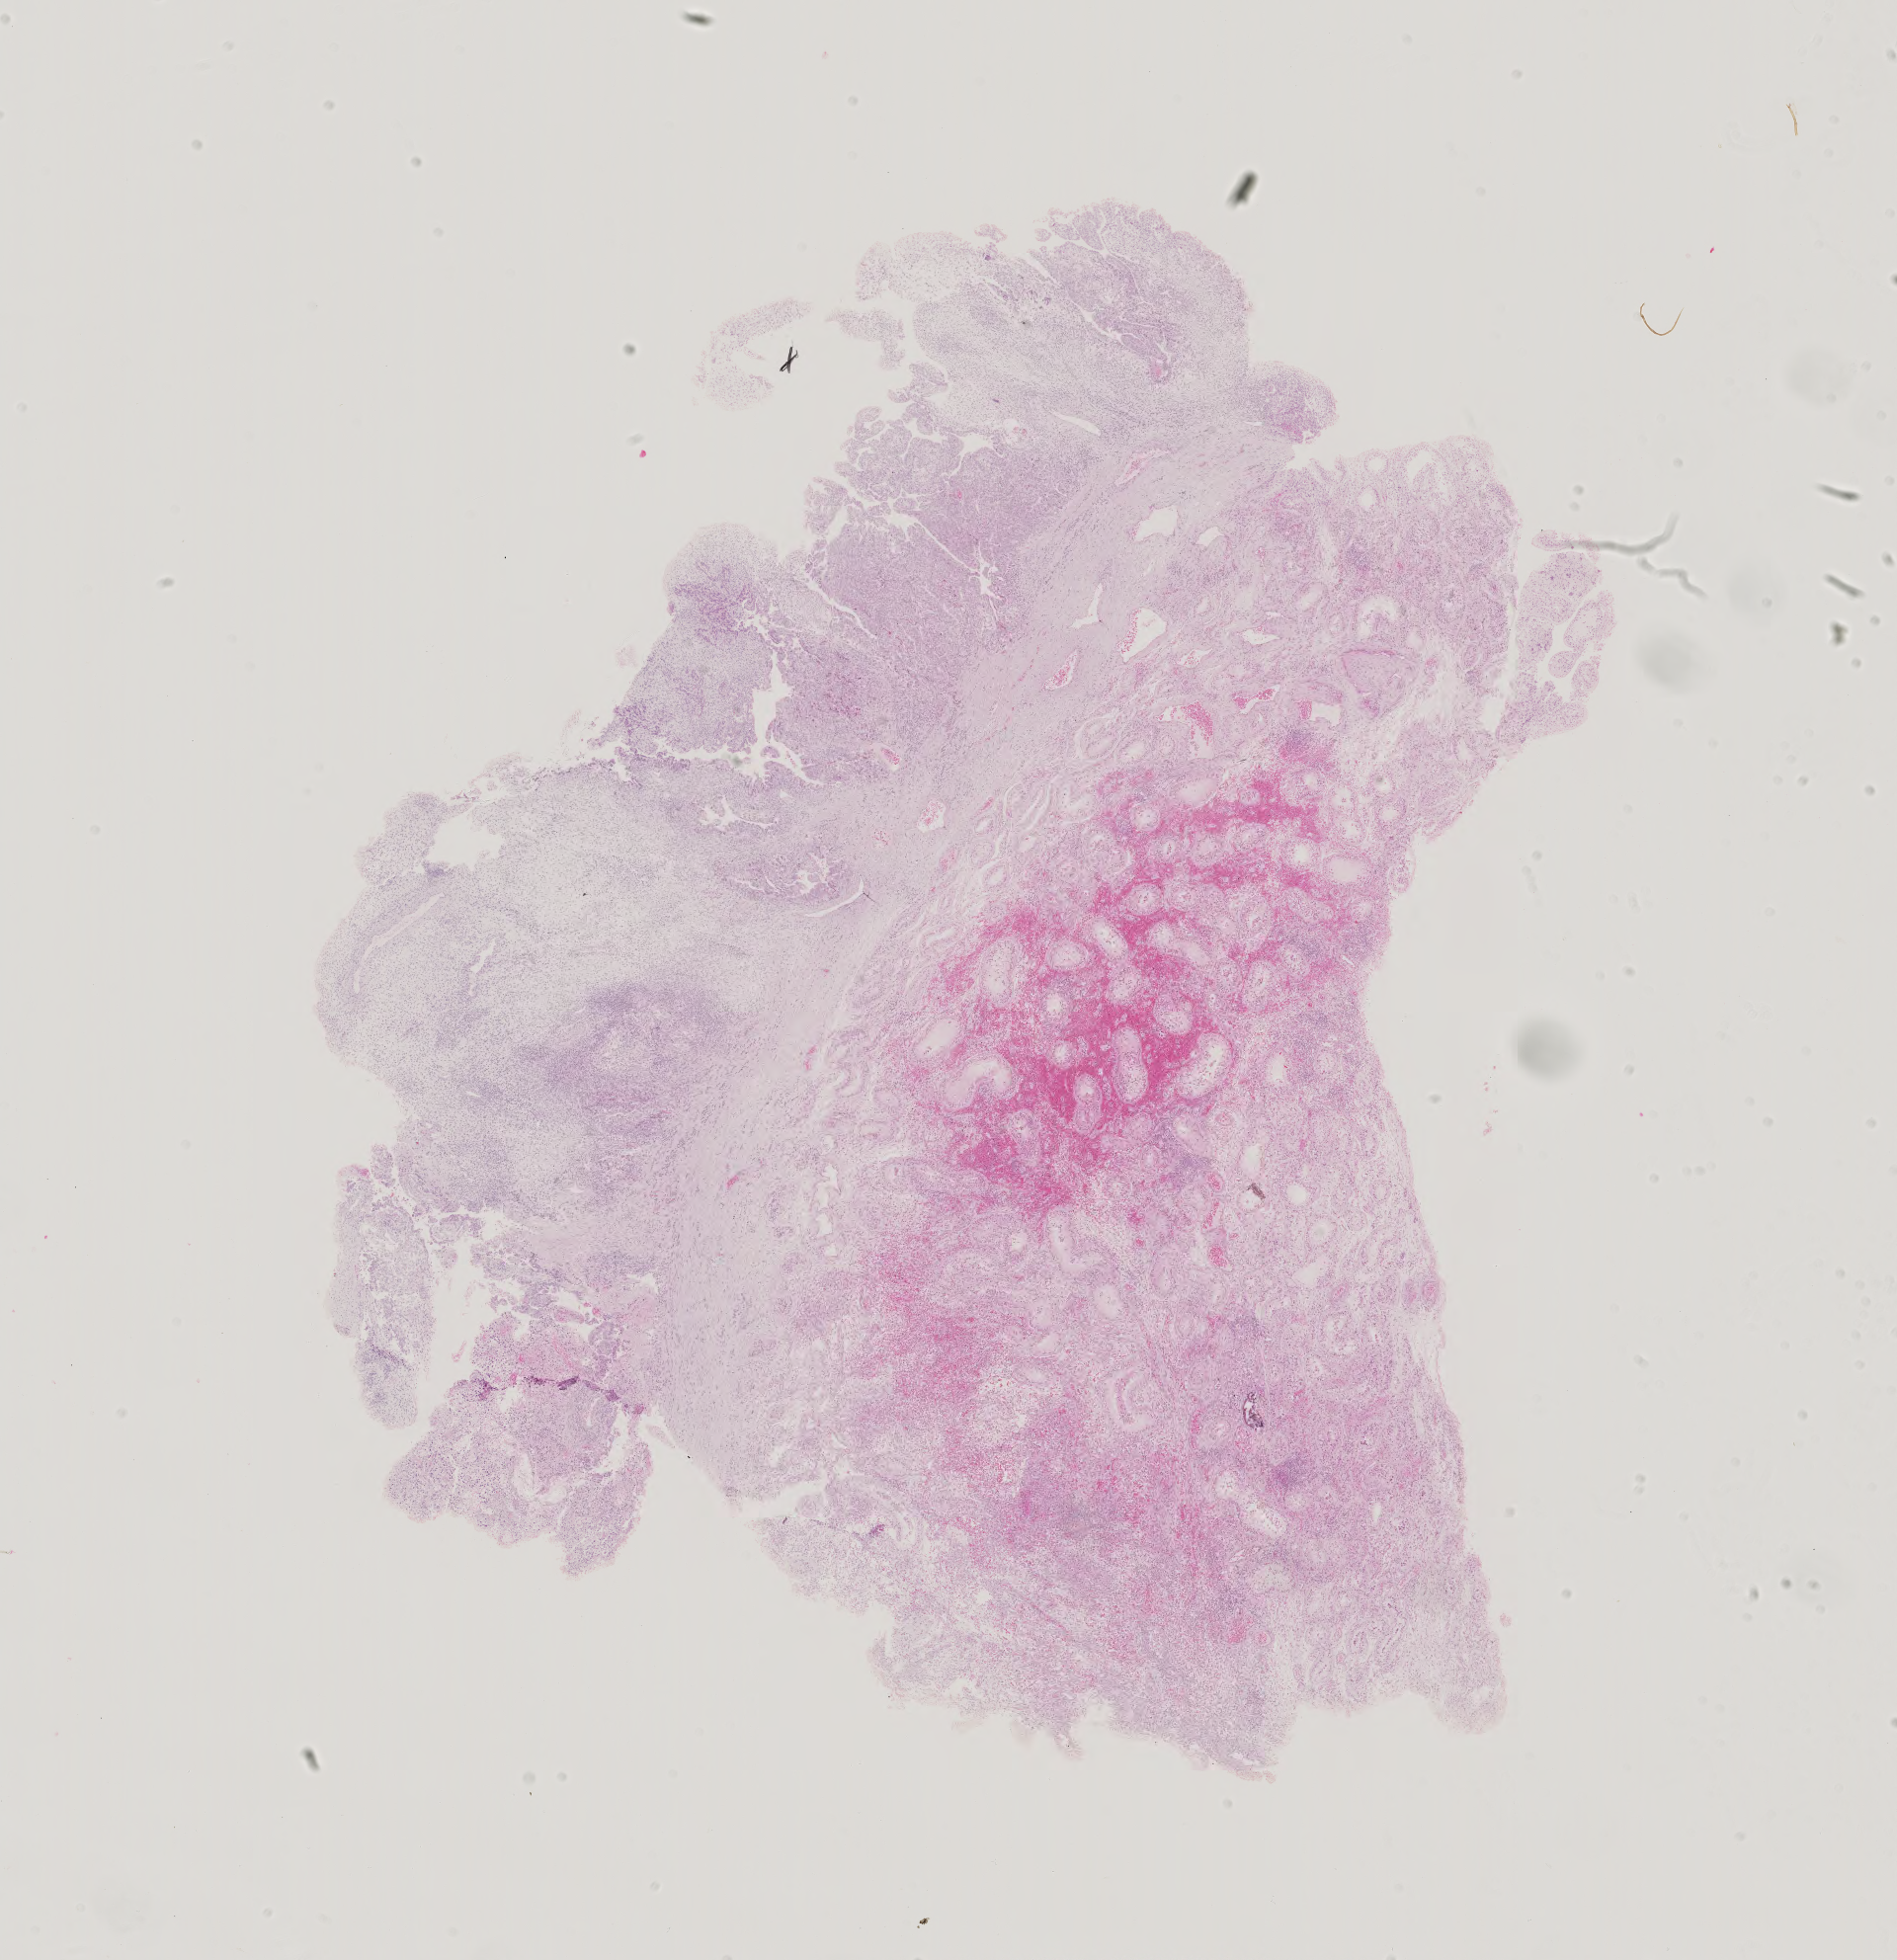
Digitized H&E-stained tissue section (whole slide) — a low-resolution overview of the entire scanned area, about 14.0 x 14.5 mm. Patient sex: male.
Specimen: formalin-fixed paraffin-embedded (FFPE) diagnostic section; sample: primary tumour, testis.